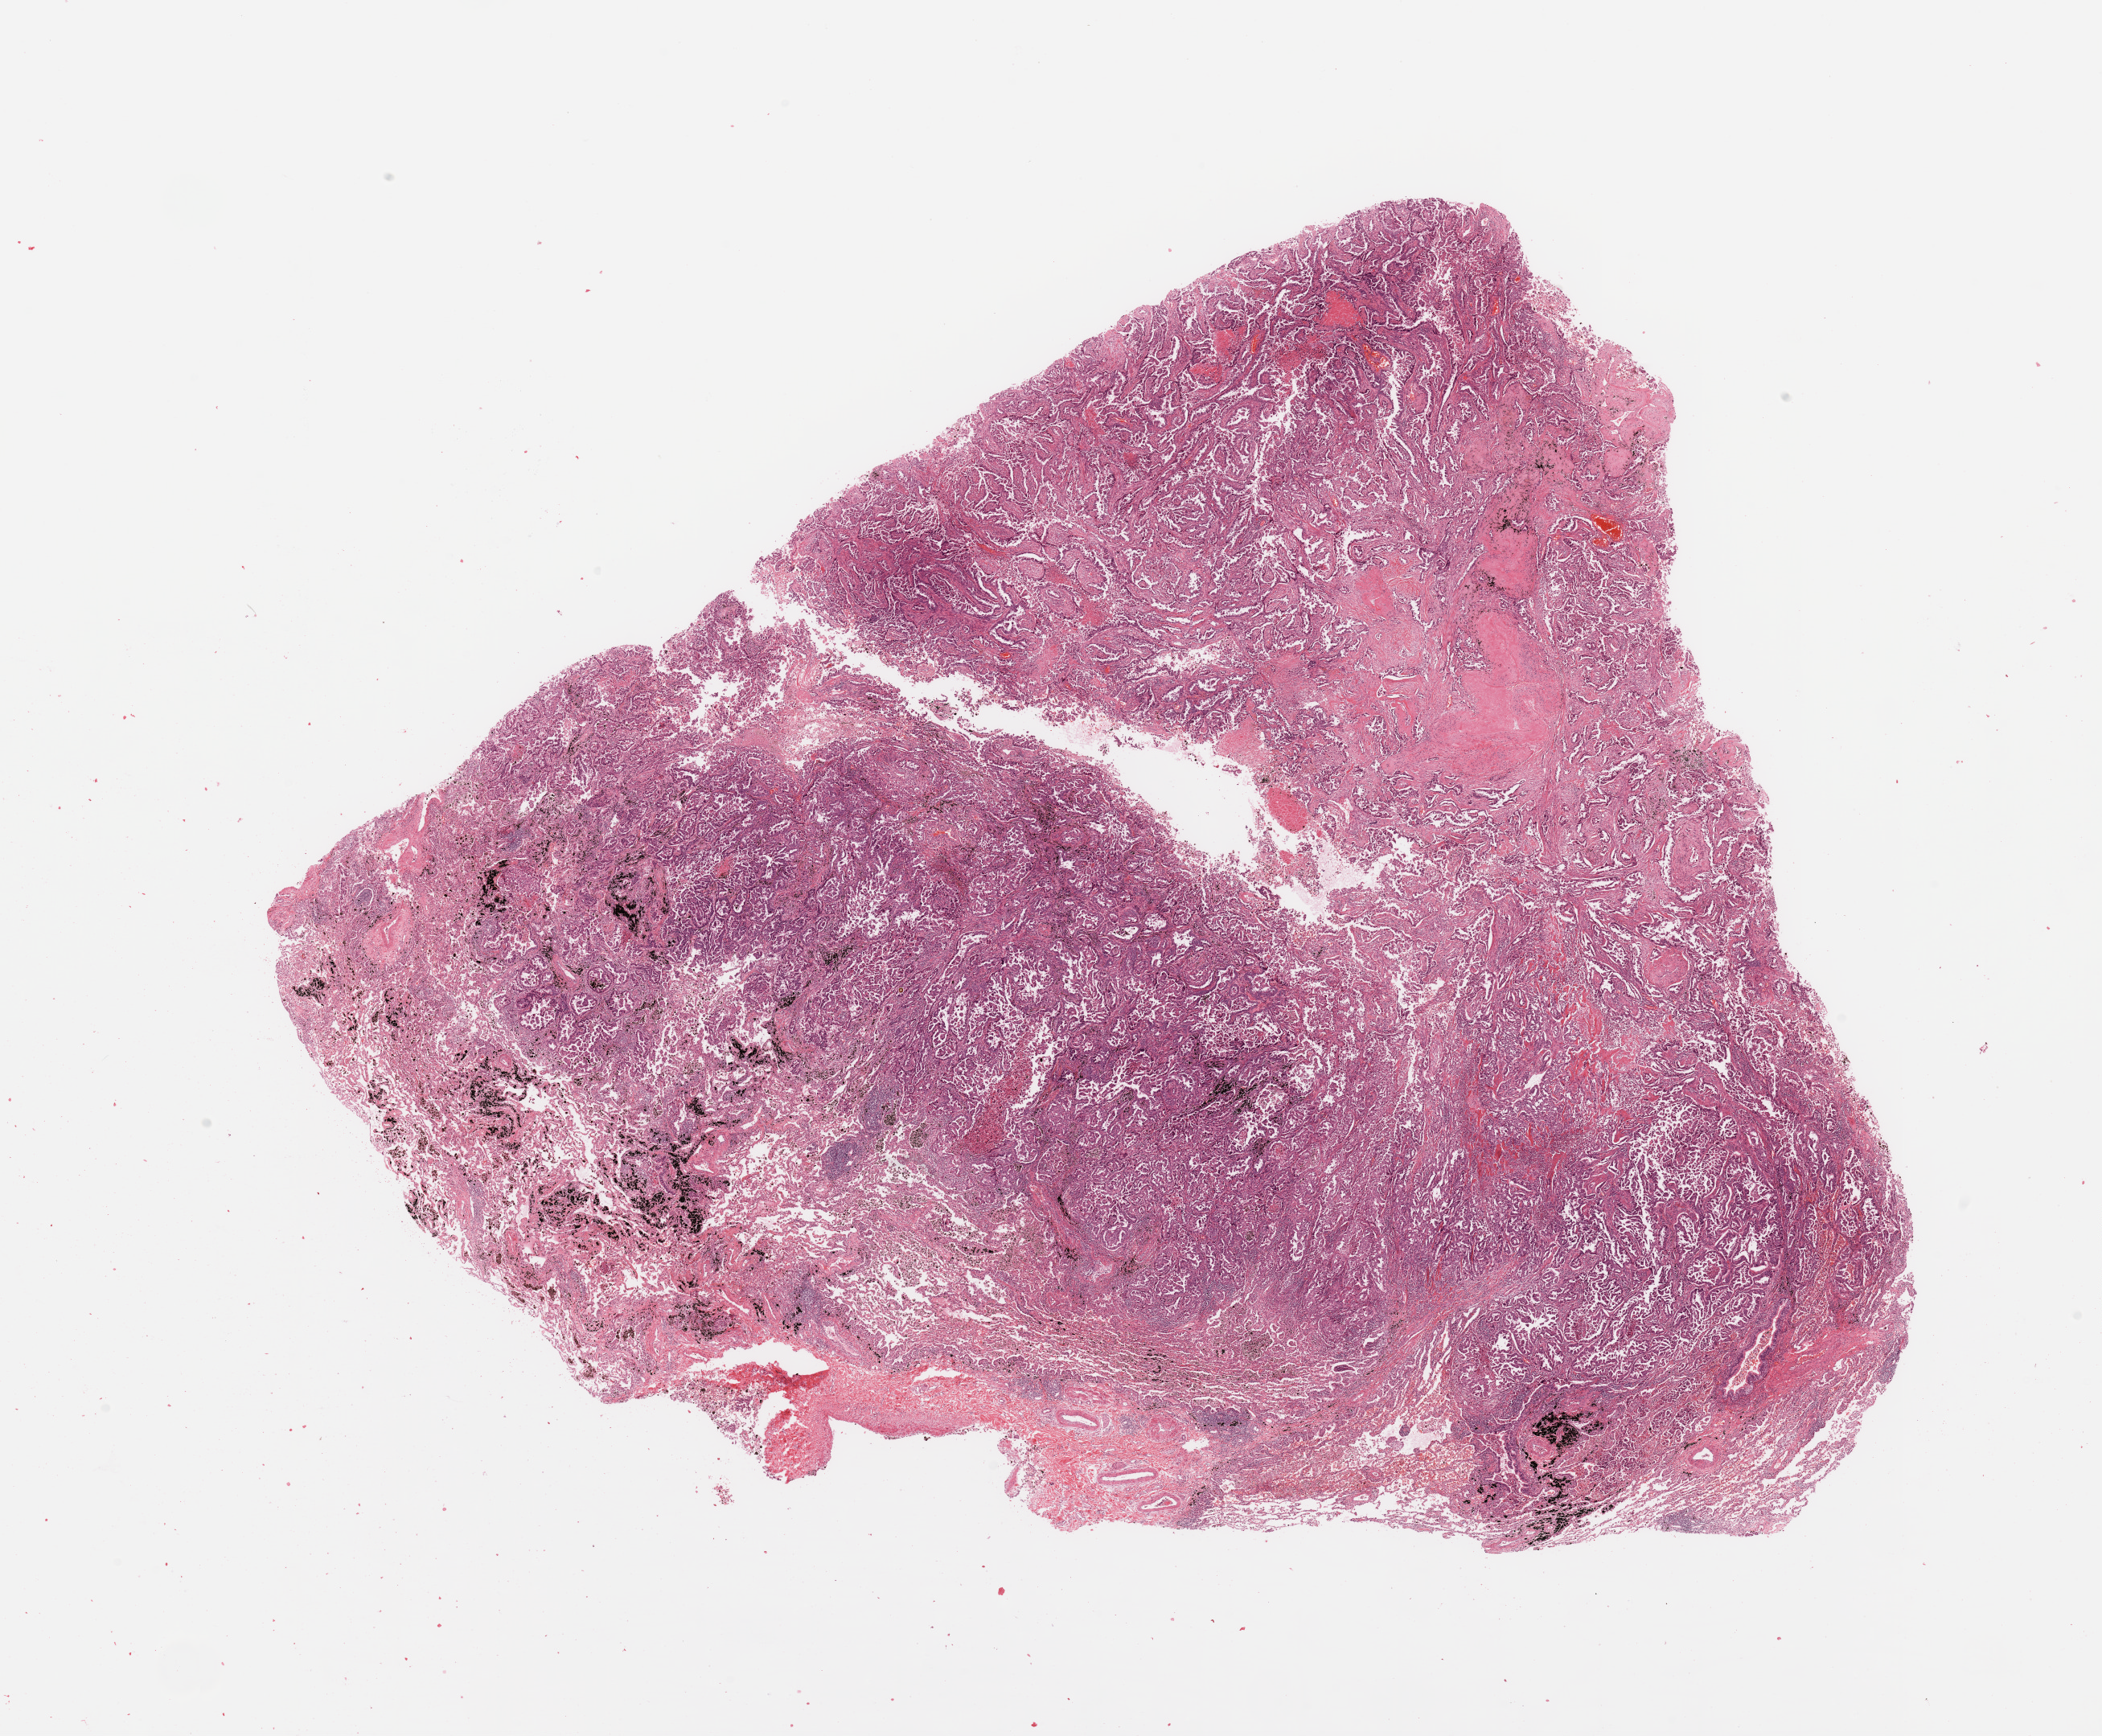
Whole-slide histology image, H&E-stained — shown as a low-resolution overview of the whole scanned area (about 20.7 x 17.1 mm). Lung, tumour tissue. Male, 56 y/o.
Histologic diagnosis: Adenocarcinoma, NOS.